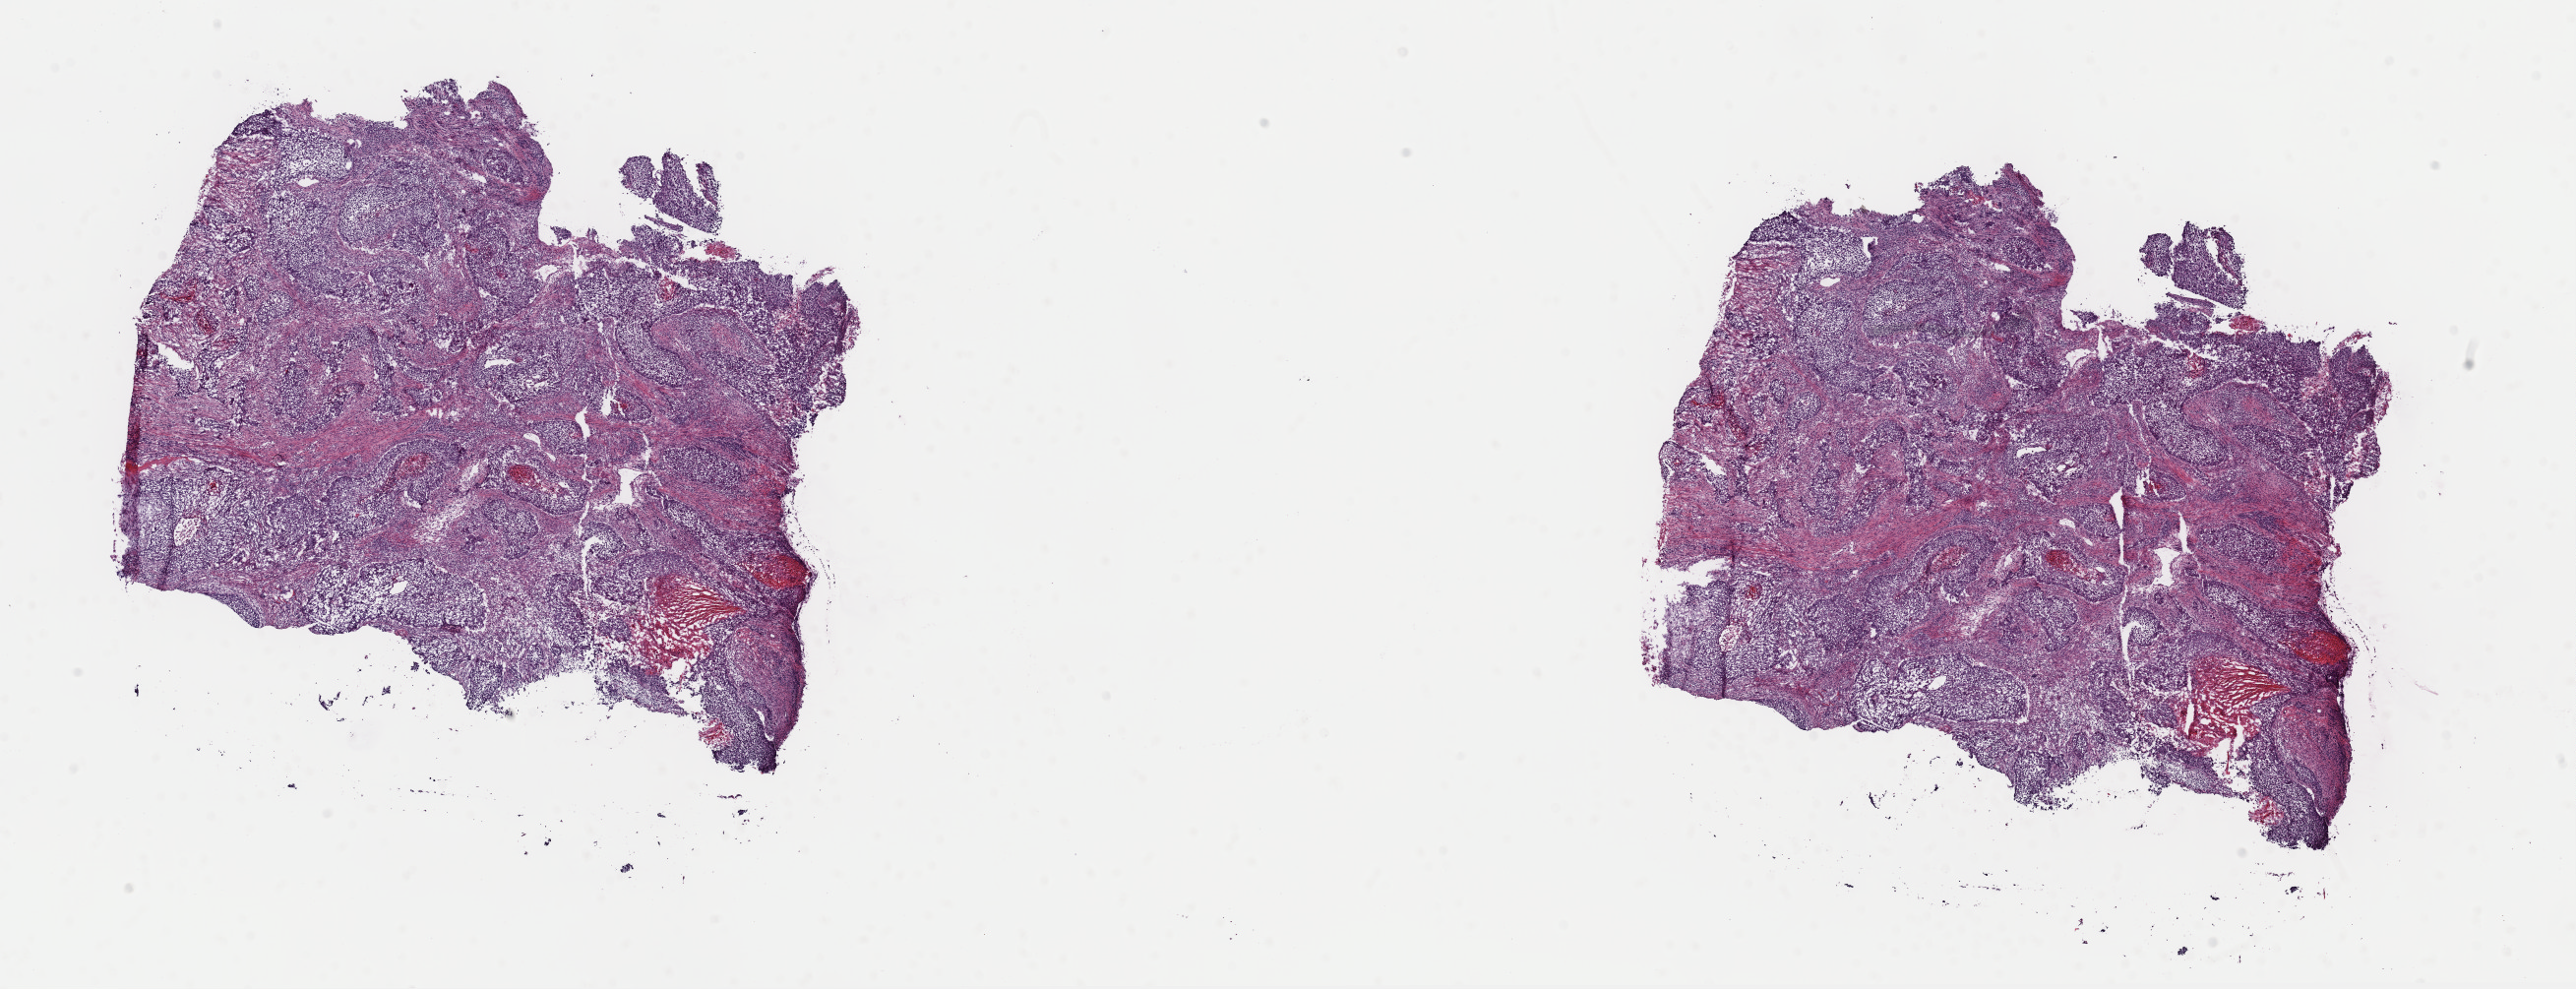
Whole-slide histology image, H&E — whole scanned area (about 20.7 x 7.9 mm) shown as a low-resolution overview; frozen section from the top of the tissue portion; sample: primary tumour, lung. Male patient; age at initial diagnosis 49 years. Slide review estimates, as recorded: tumour cells 70%, tumour nuclei 80%, normal cells 0%, stromal cells 20%, necrosis 10%. Inflammatory infiltration, as recorded: lymphocyte infiltration 0%, monocyte infiltration 0%, neutrophil infiltration 0%.
- AJCC pathologic stage: II
- histologic diagnosis: Squamous cell carcinoma, NOS (upper lobe, lung)
- laterality: left